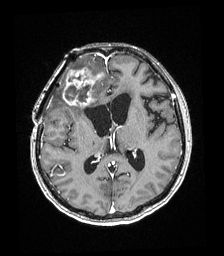
Brain MRI from a brain-tumour surgery series, one axial slice; position 92 of 192 along the scan axis; T1-weighted post-contrast; 1 mm slice thickness; 224 × 256 image matrix. From the clinical record (not read from this slice): histopathology: Astrocytoma; WHO grade: 4; IDH mutation: yes; tumour location: Right superficial frontal.
Outlined on this slice (manually delineated by an expert):
- tumour: box from (x=62, y=61) to (x=102, y=106) px